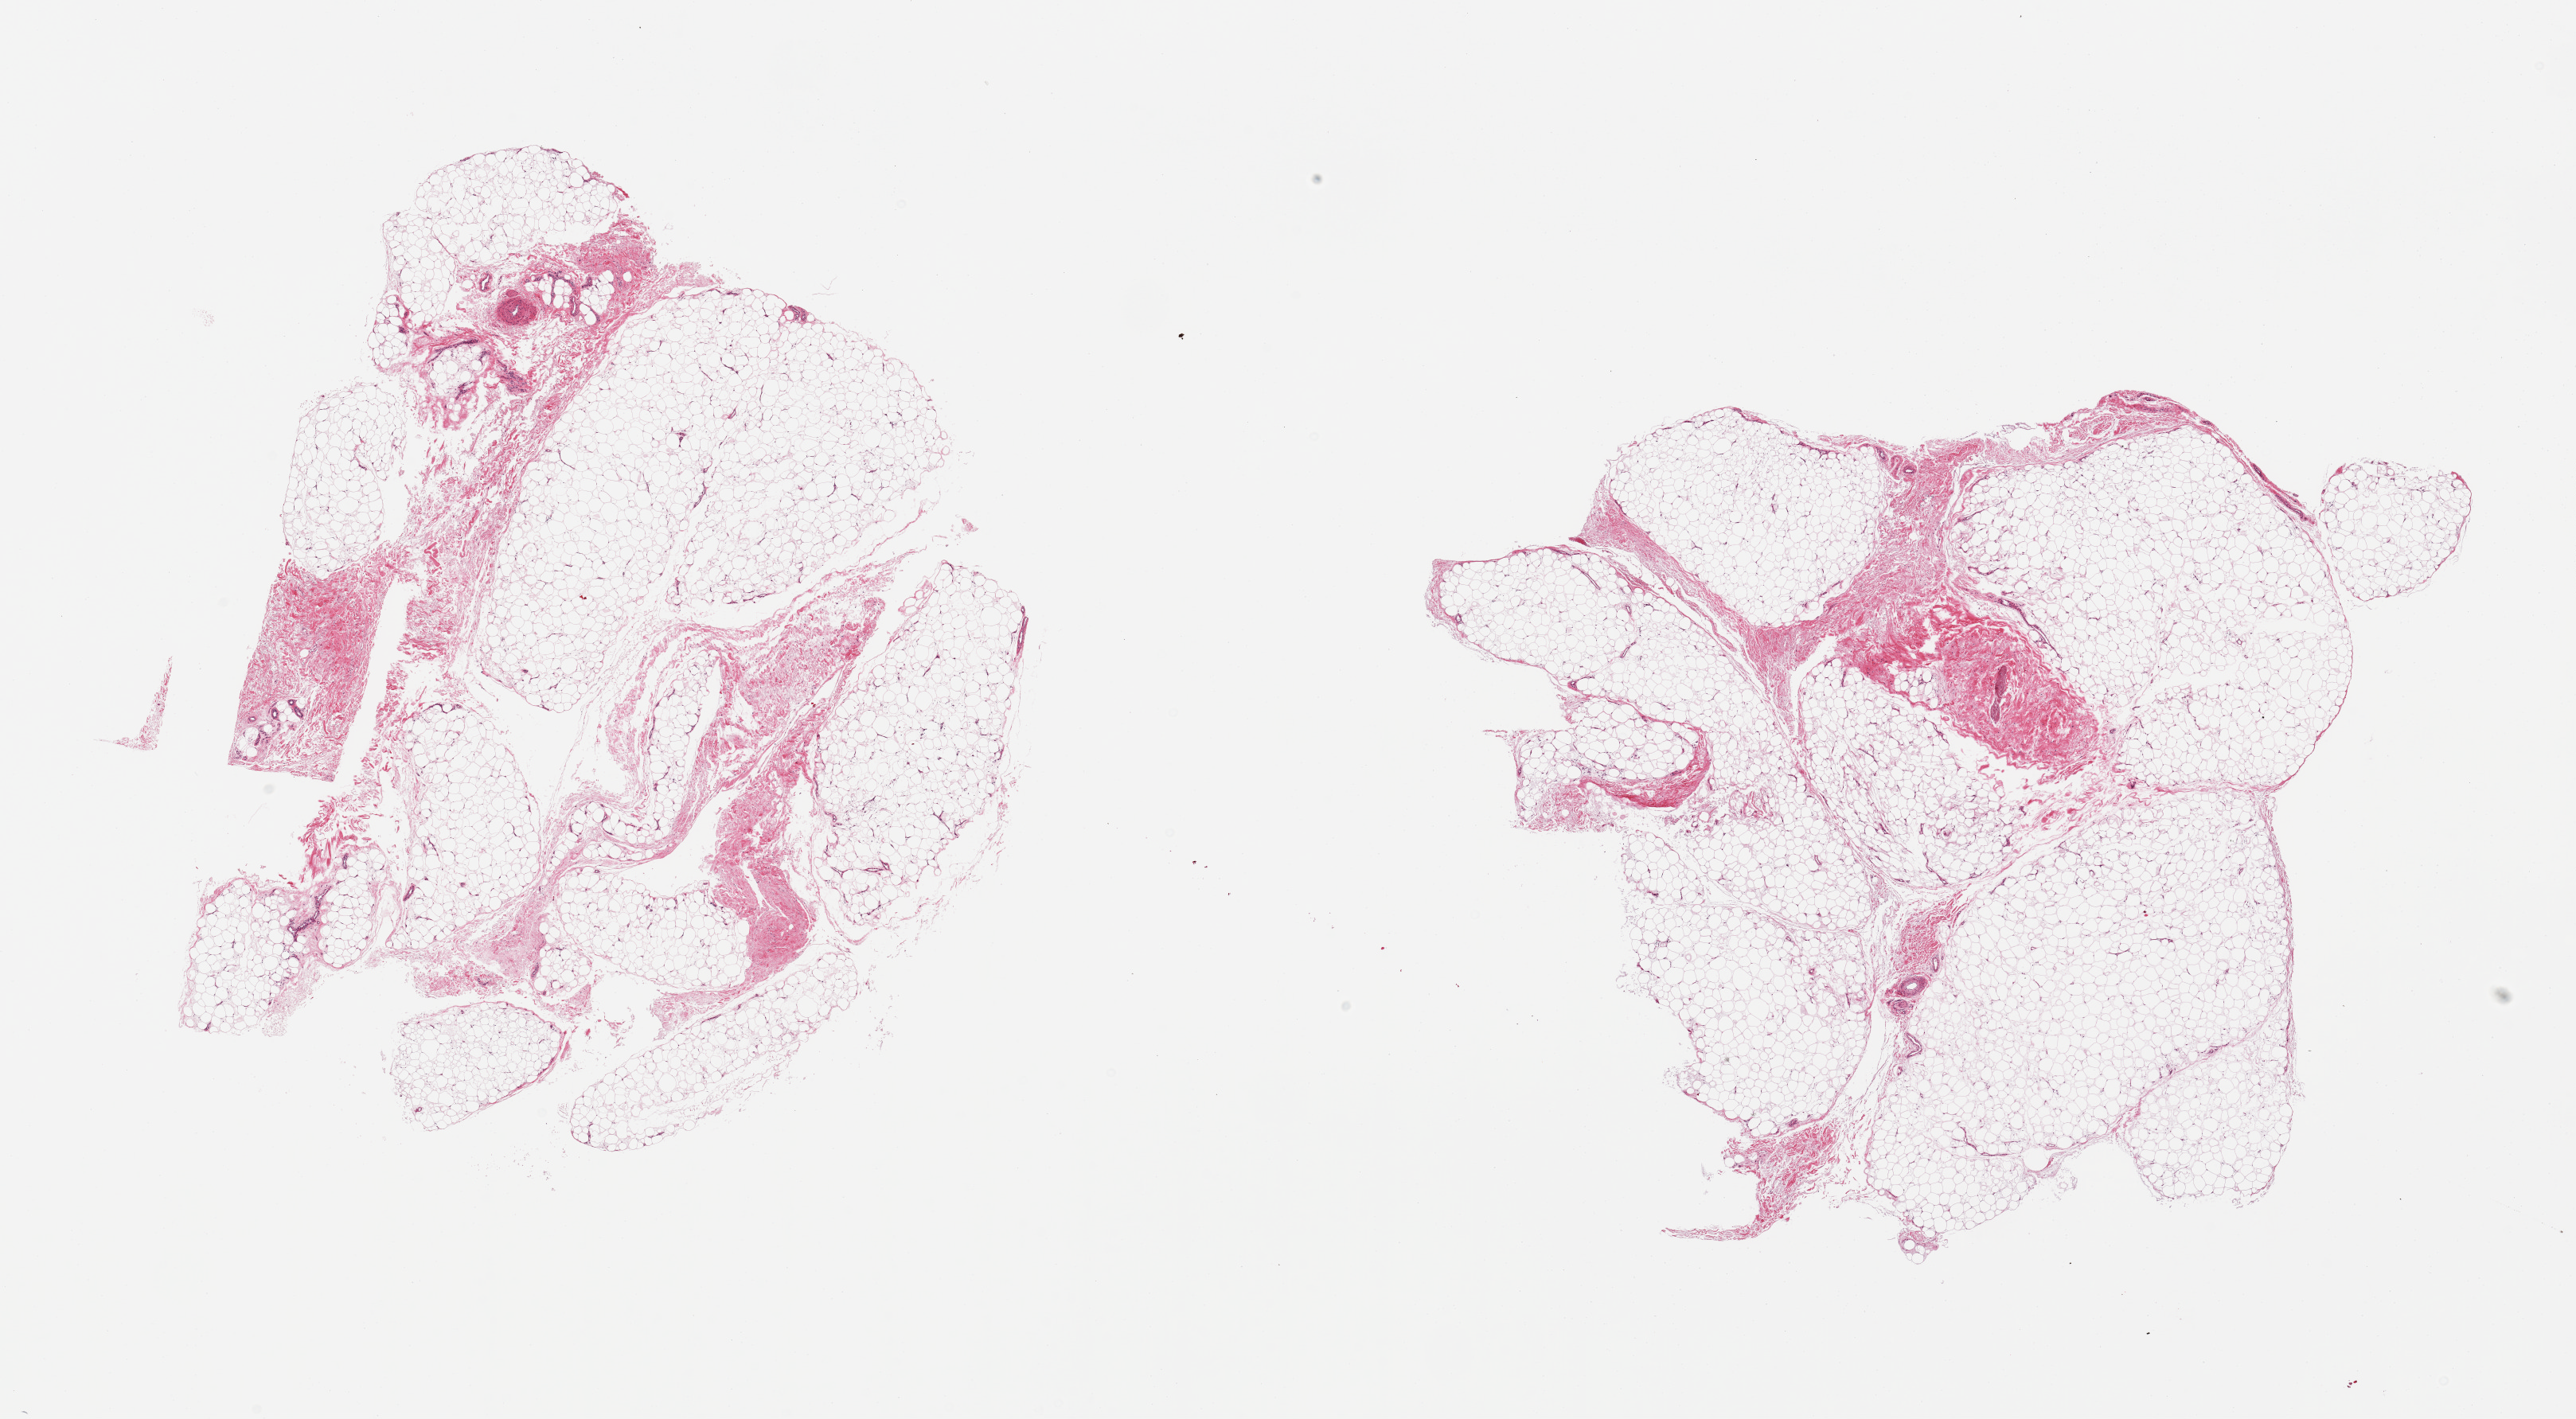
Digitized haematoxylin and eosin-stained section — low-resolution overview of the scanned area, about 25.6 x 14.1 mm (slide scanned at 20x). PAXgene-fixed, paraffin-embedded tissue. Sampled site (target tissue): adipose tissue. Donor tissue sample. Donor sex: male.
Review note (as recorded): 2 pieces; mature adipose tissue and ~25% fibrovascular component.